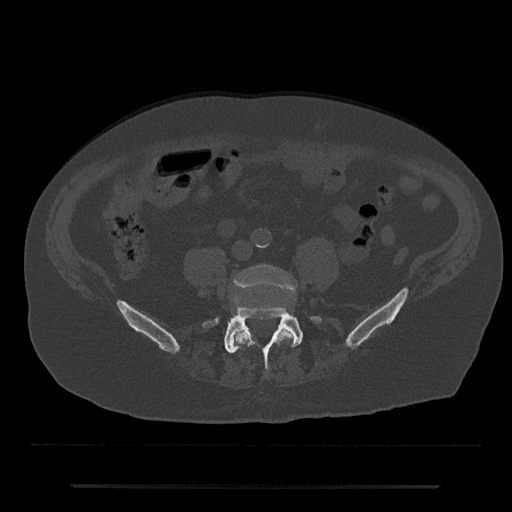
CT including the spine, one axial slice. Position 311 of 797 along the scan axis. Reconstruction kernel Br40s/3. Bone window (W 1800 / L 400 HU). 0.5 mm slice thickness. 512 × 512 image matrix, field of view 434 × 434 mm. Patient: male, 80 years. From the clinical record (not read from this slice): primary cancer: prostate.
Structures marked on this image (semi-automatic segmentation, software-assisted and operator-edited):
- L4 vertebra: bounding box [x1, y1, x2, y2] px = [233, 265, 296, 346]
- L5 vertebra: [203, 307, 321, 370]